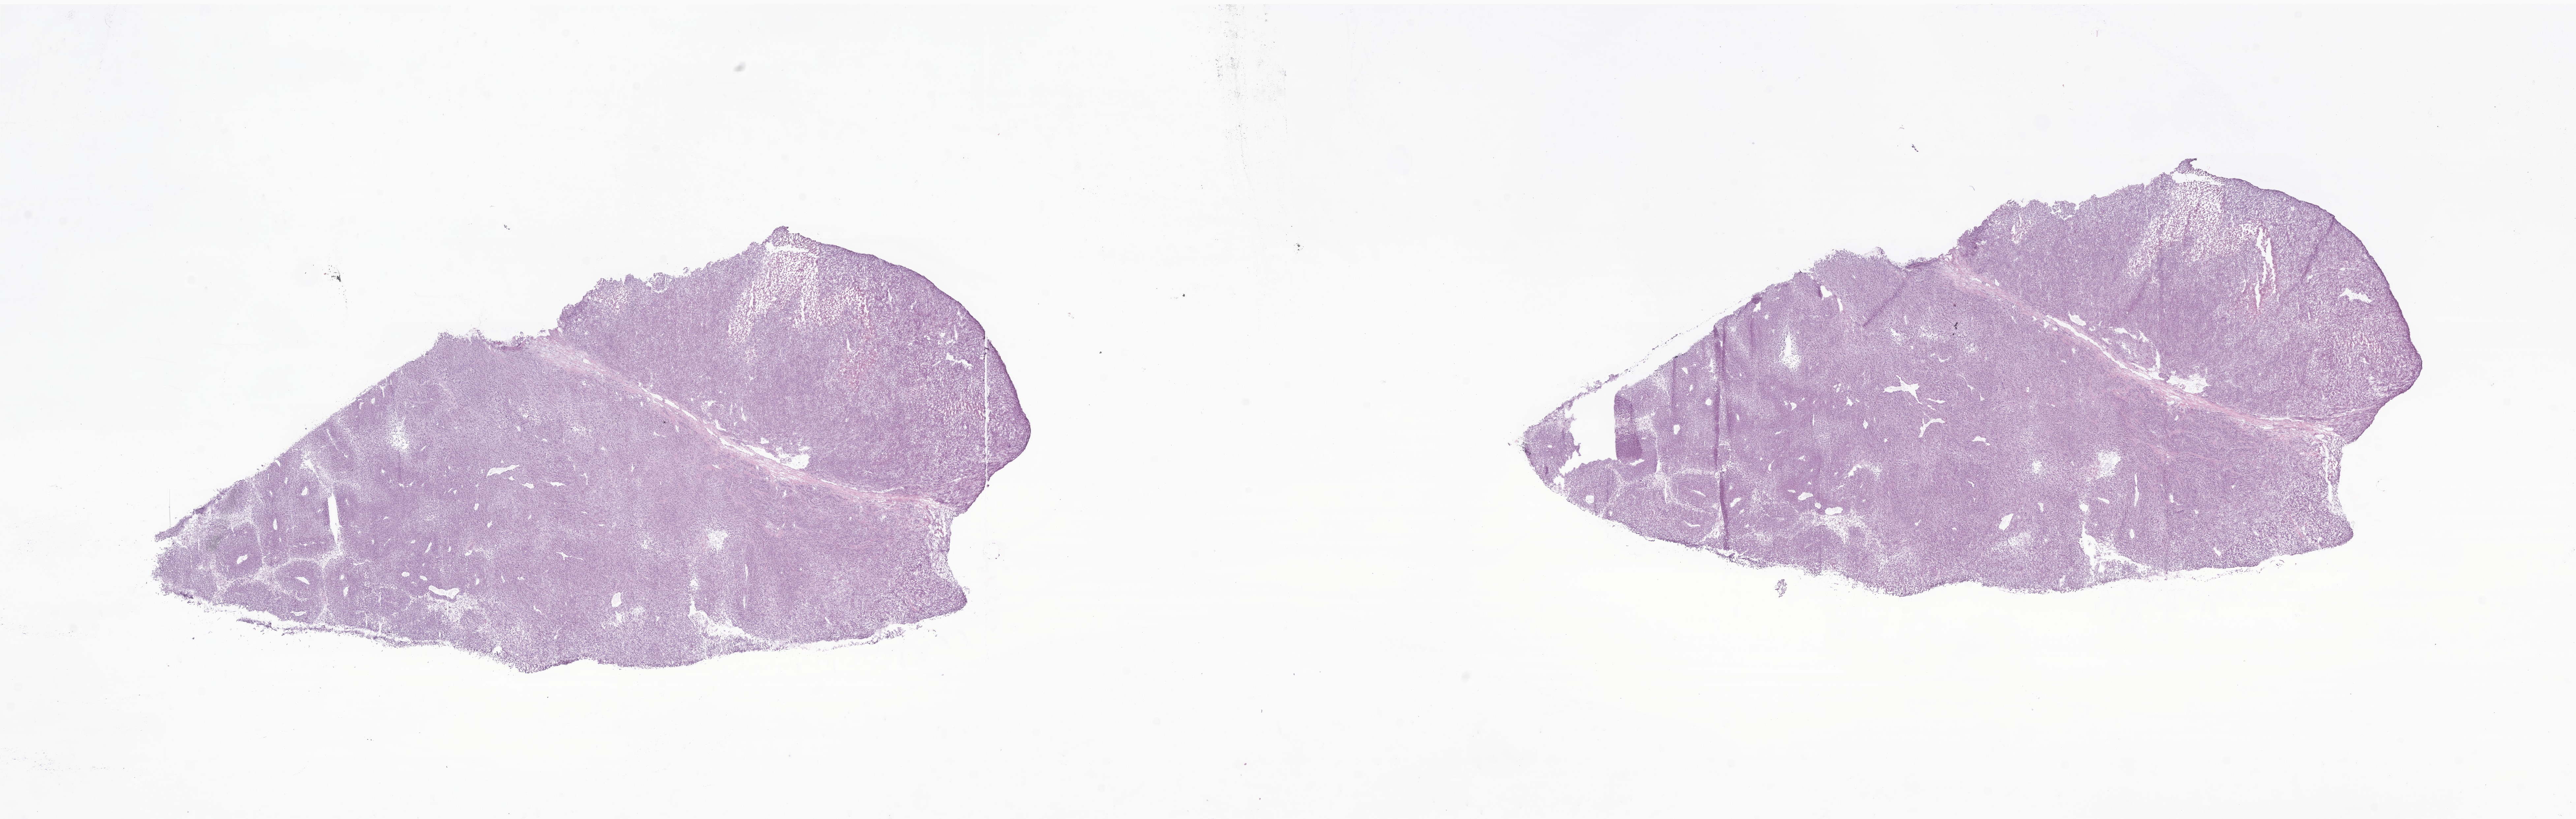
Digitized H&E-stained section of tumor tissue from the adrenal gland, low-resolution overview of the scanned area, about 32.9 x 10.5 mm, cryosection (OCT / tissue freezing medium). Patient male; age 143 months (11 years 11 months).
* diagnosis: Adenocarcinoma, NOS